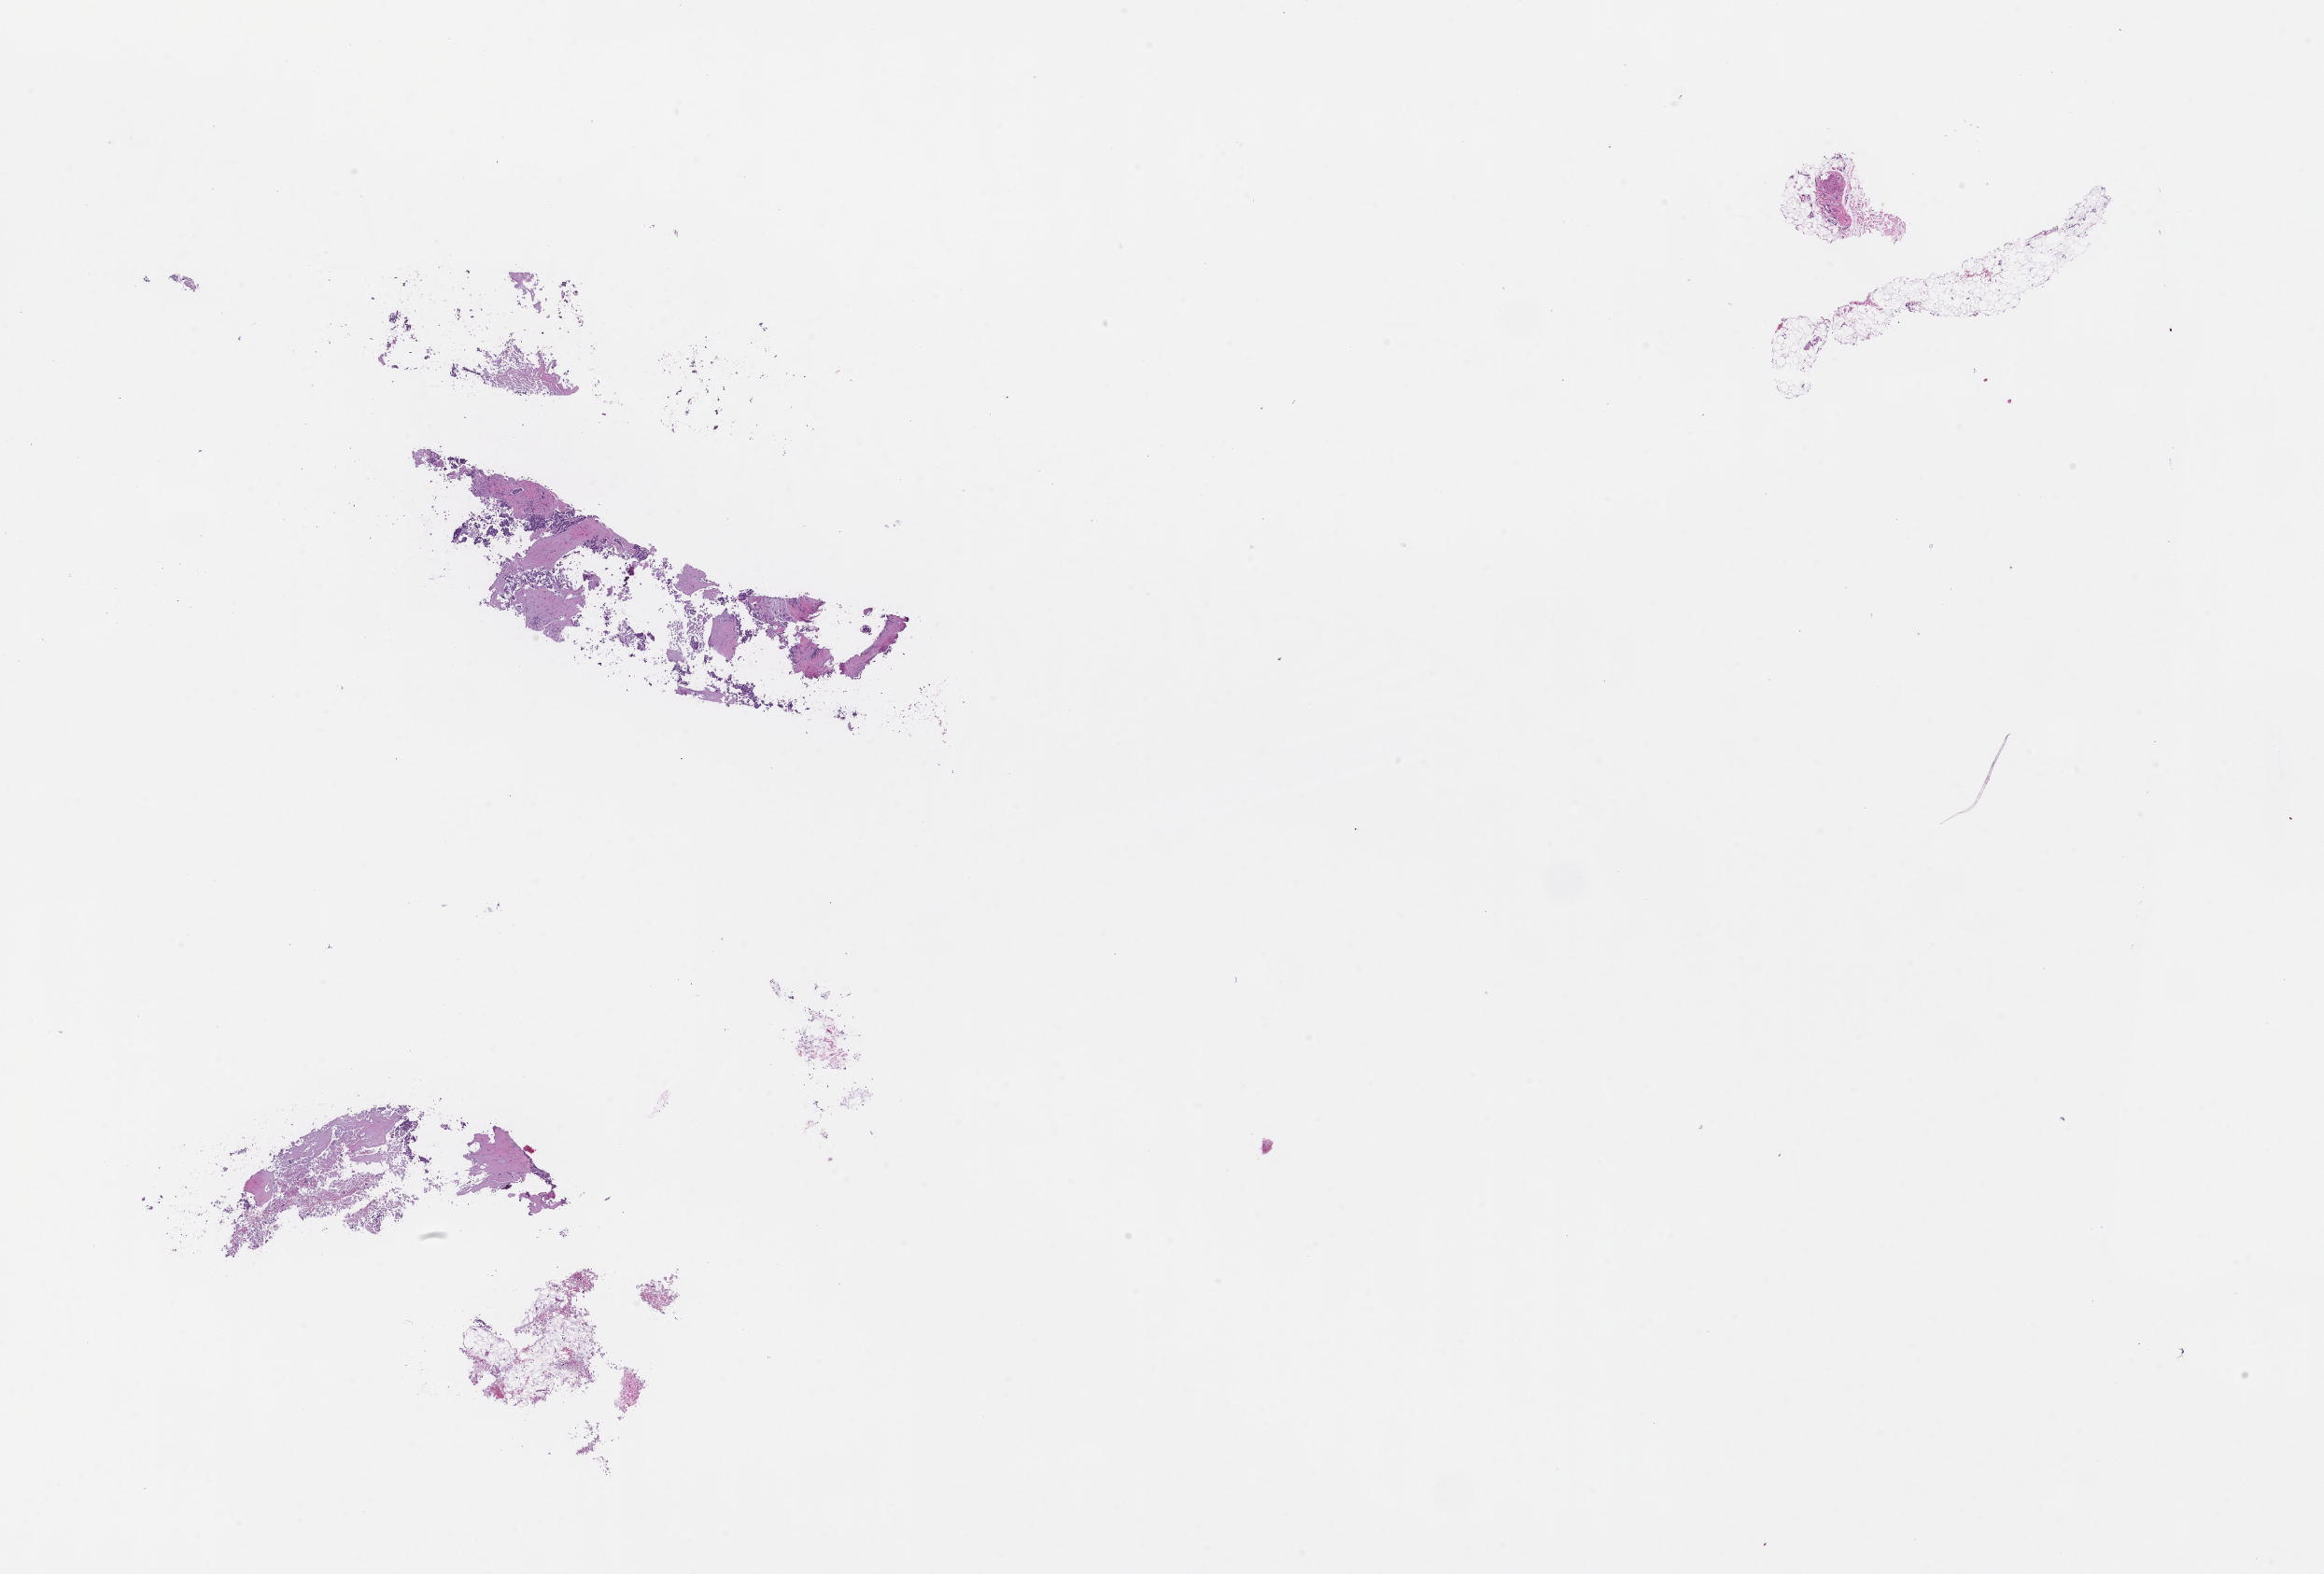
H&E whole-slide image — low-resolution overview of the scanned area, about 20.1 x 13.6 mm; FFPE section; site: breast; archival tissue. Patient: female.
This section: primary tumor. Diagnosis: Invasive Breast Carcinoma.